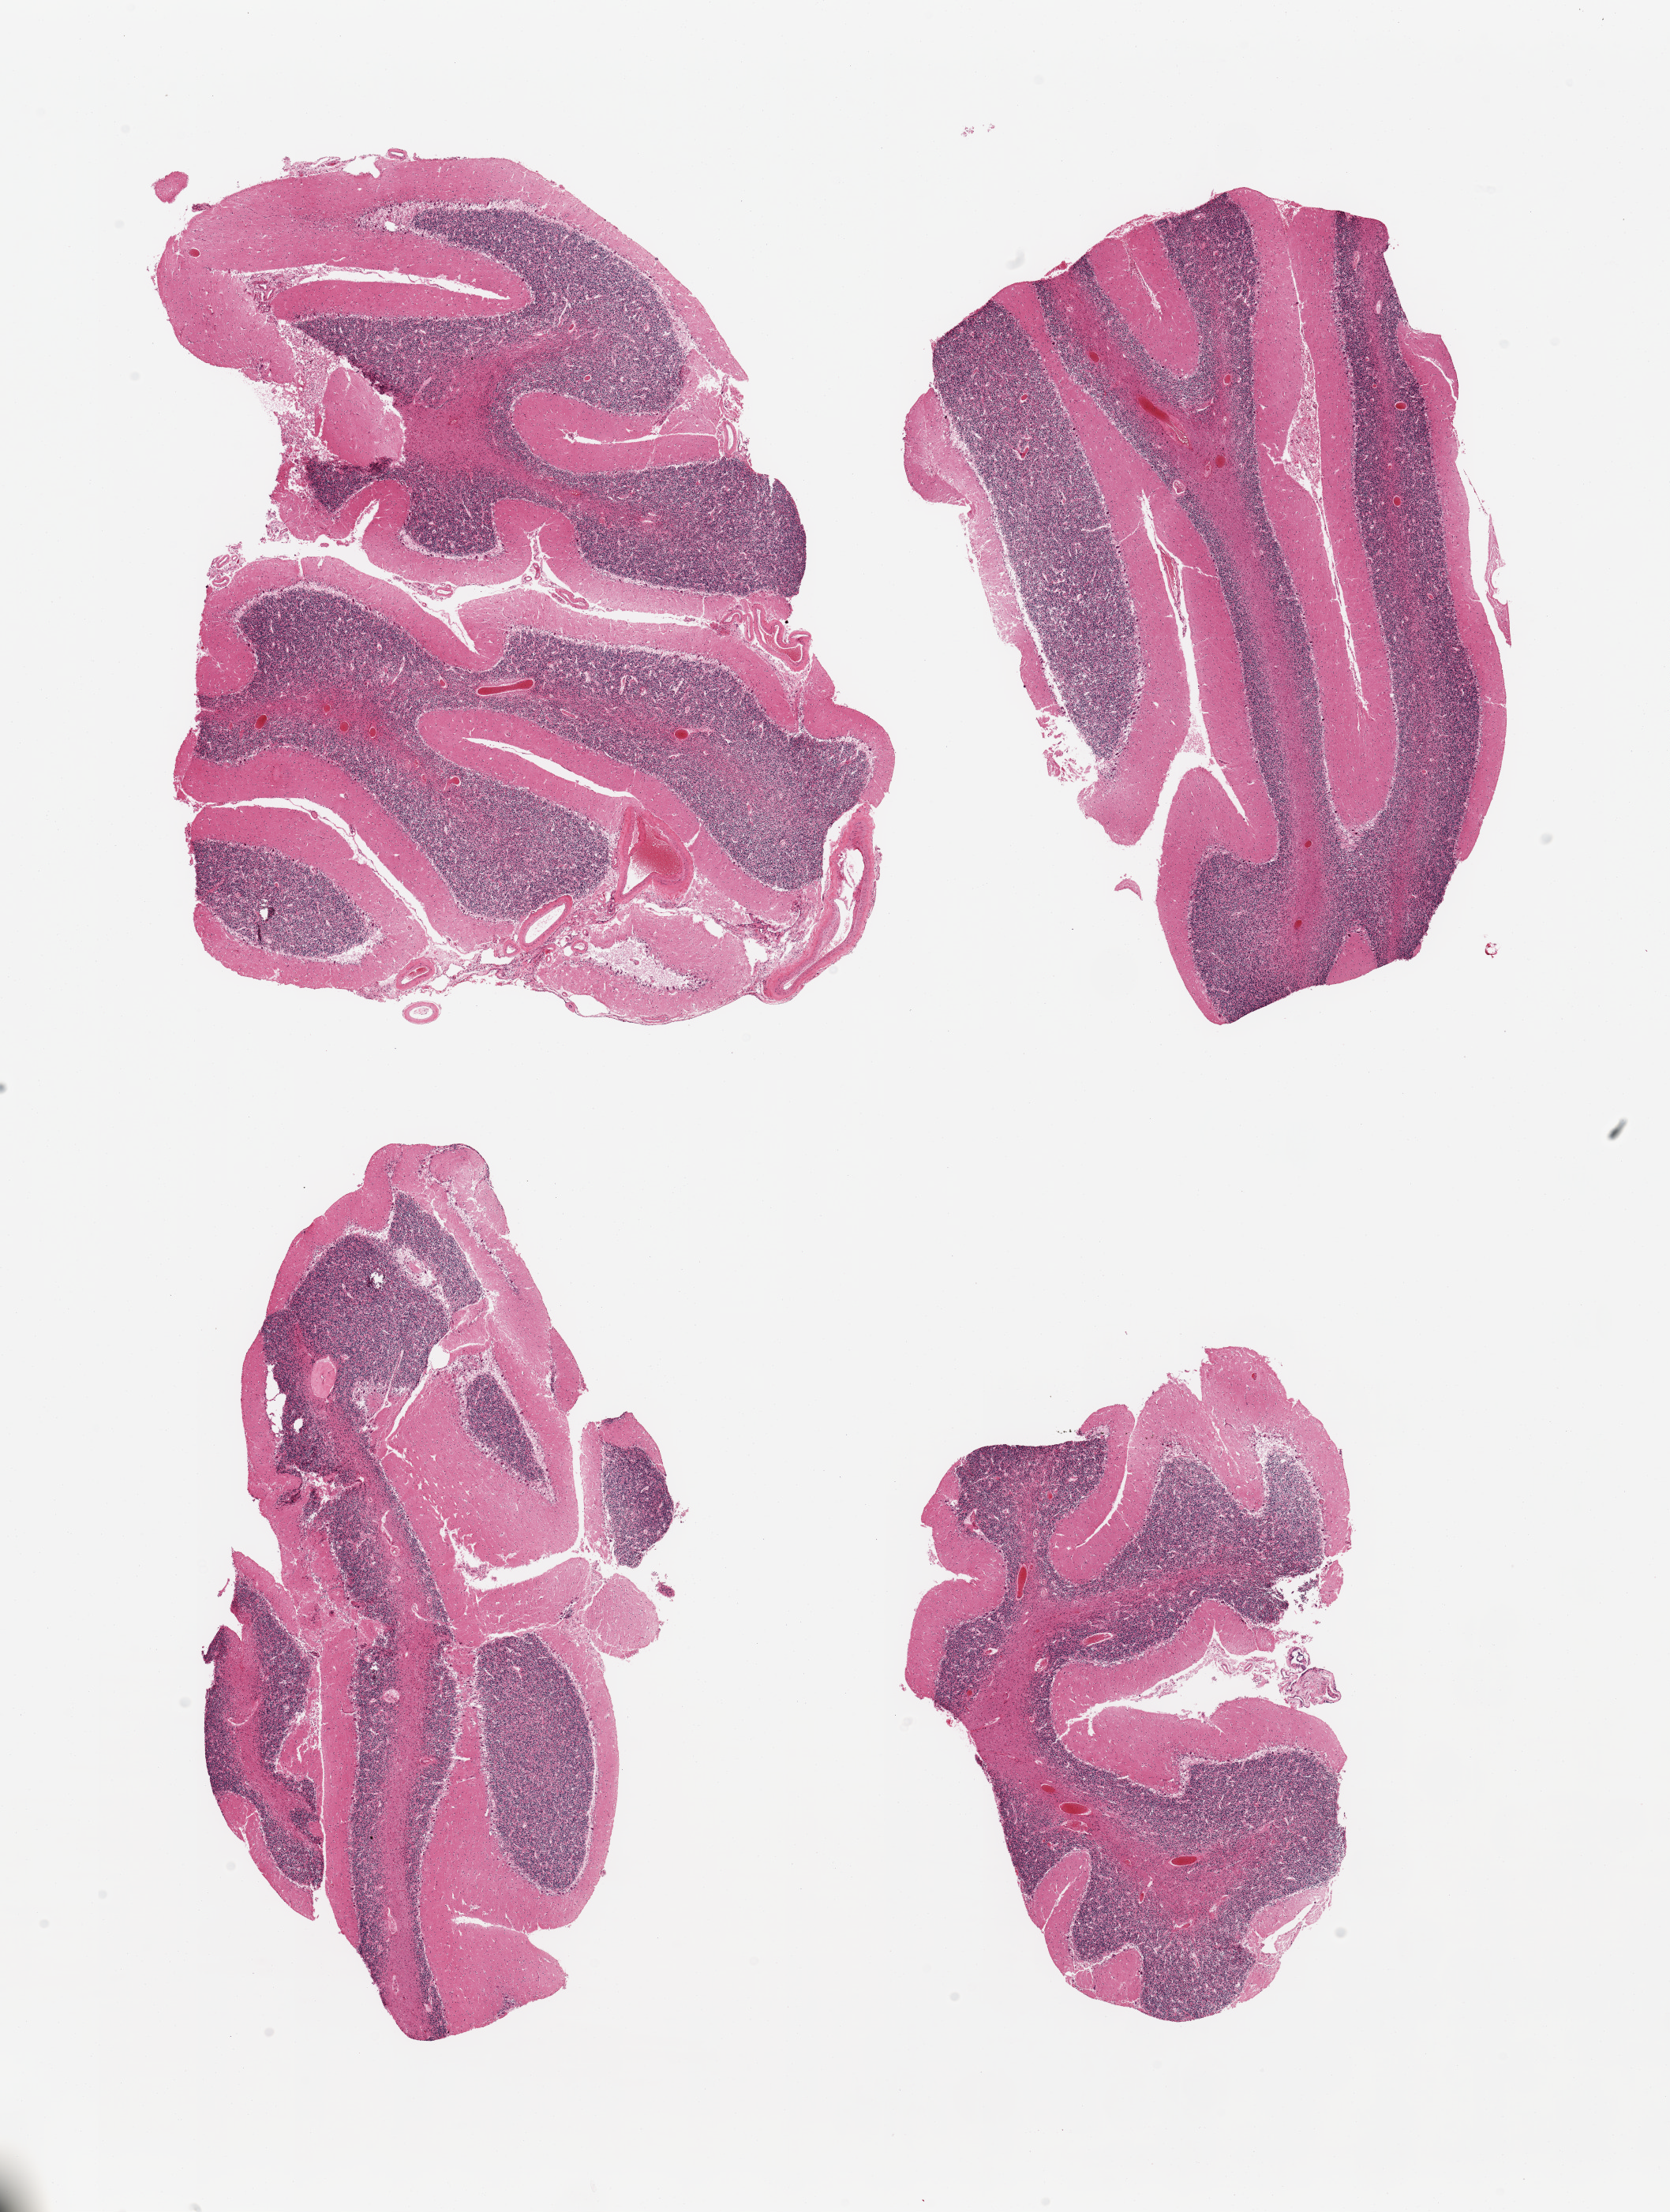
Hematoxylin and eosin (H&E) whole-slide image — low-resolution overview of the scanned area, about 16.7 x 22.2 mm. PAXgene-fixed paraffin-embedded (PFPE) section. Target tissue: cerebellum. Tissue donor sample. Male donor.
Review note (as recorded): 4 pieces, no abnormalities.